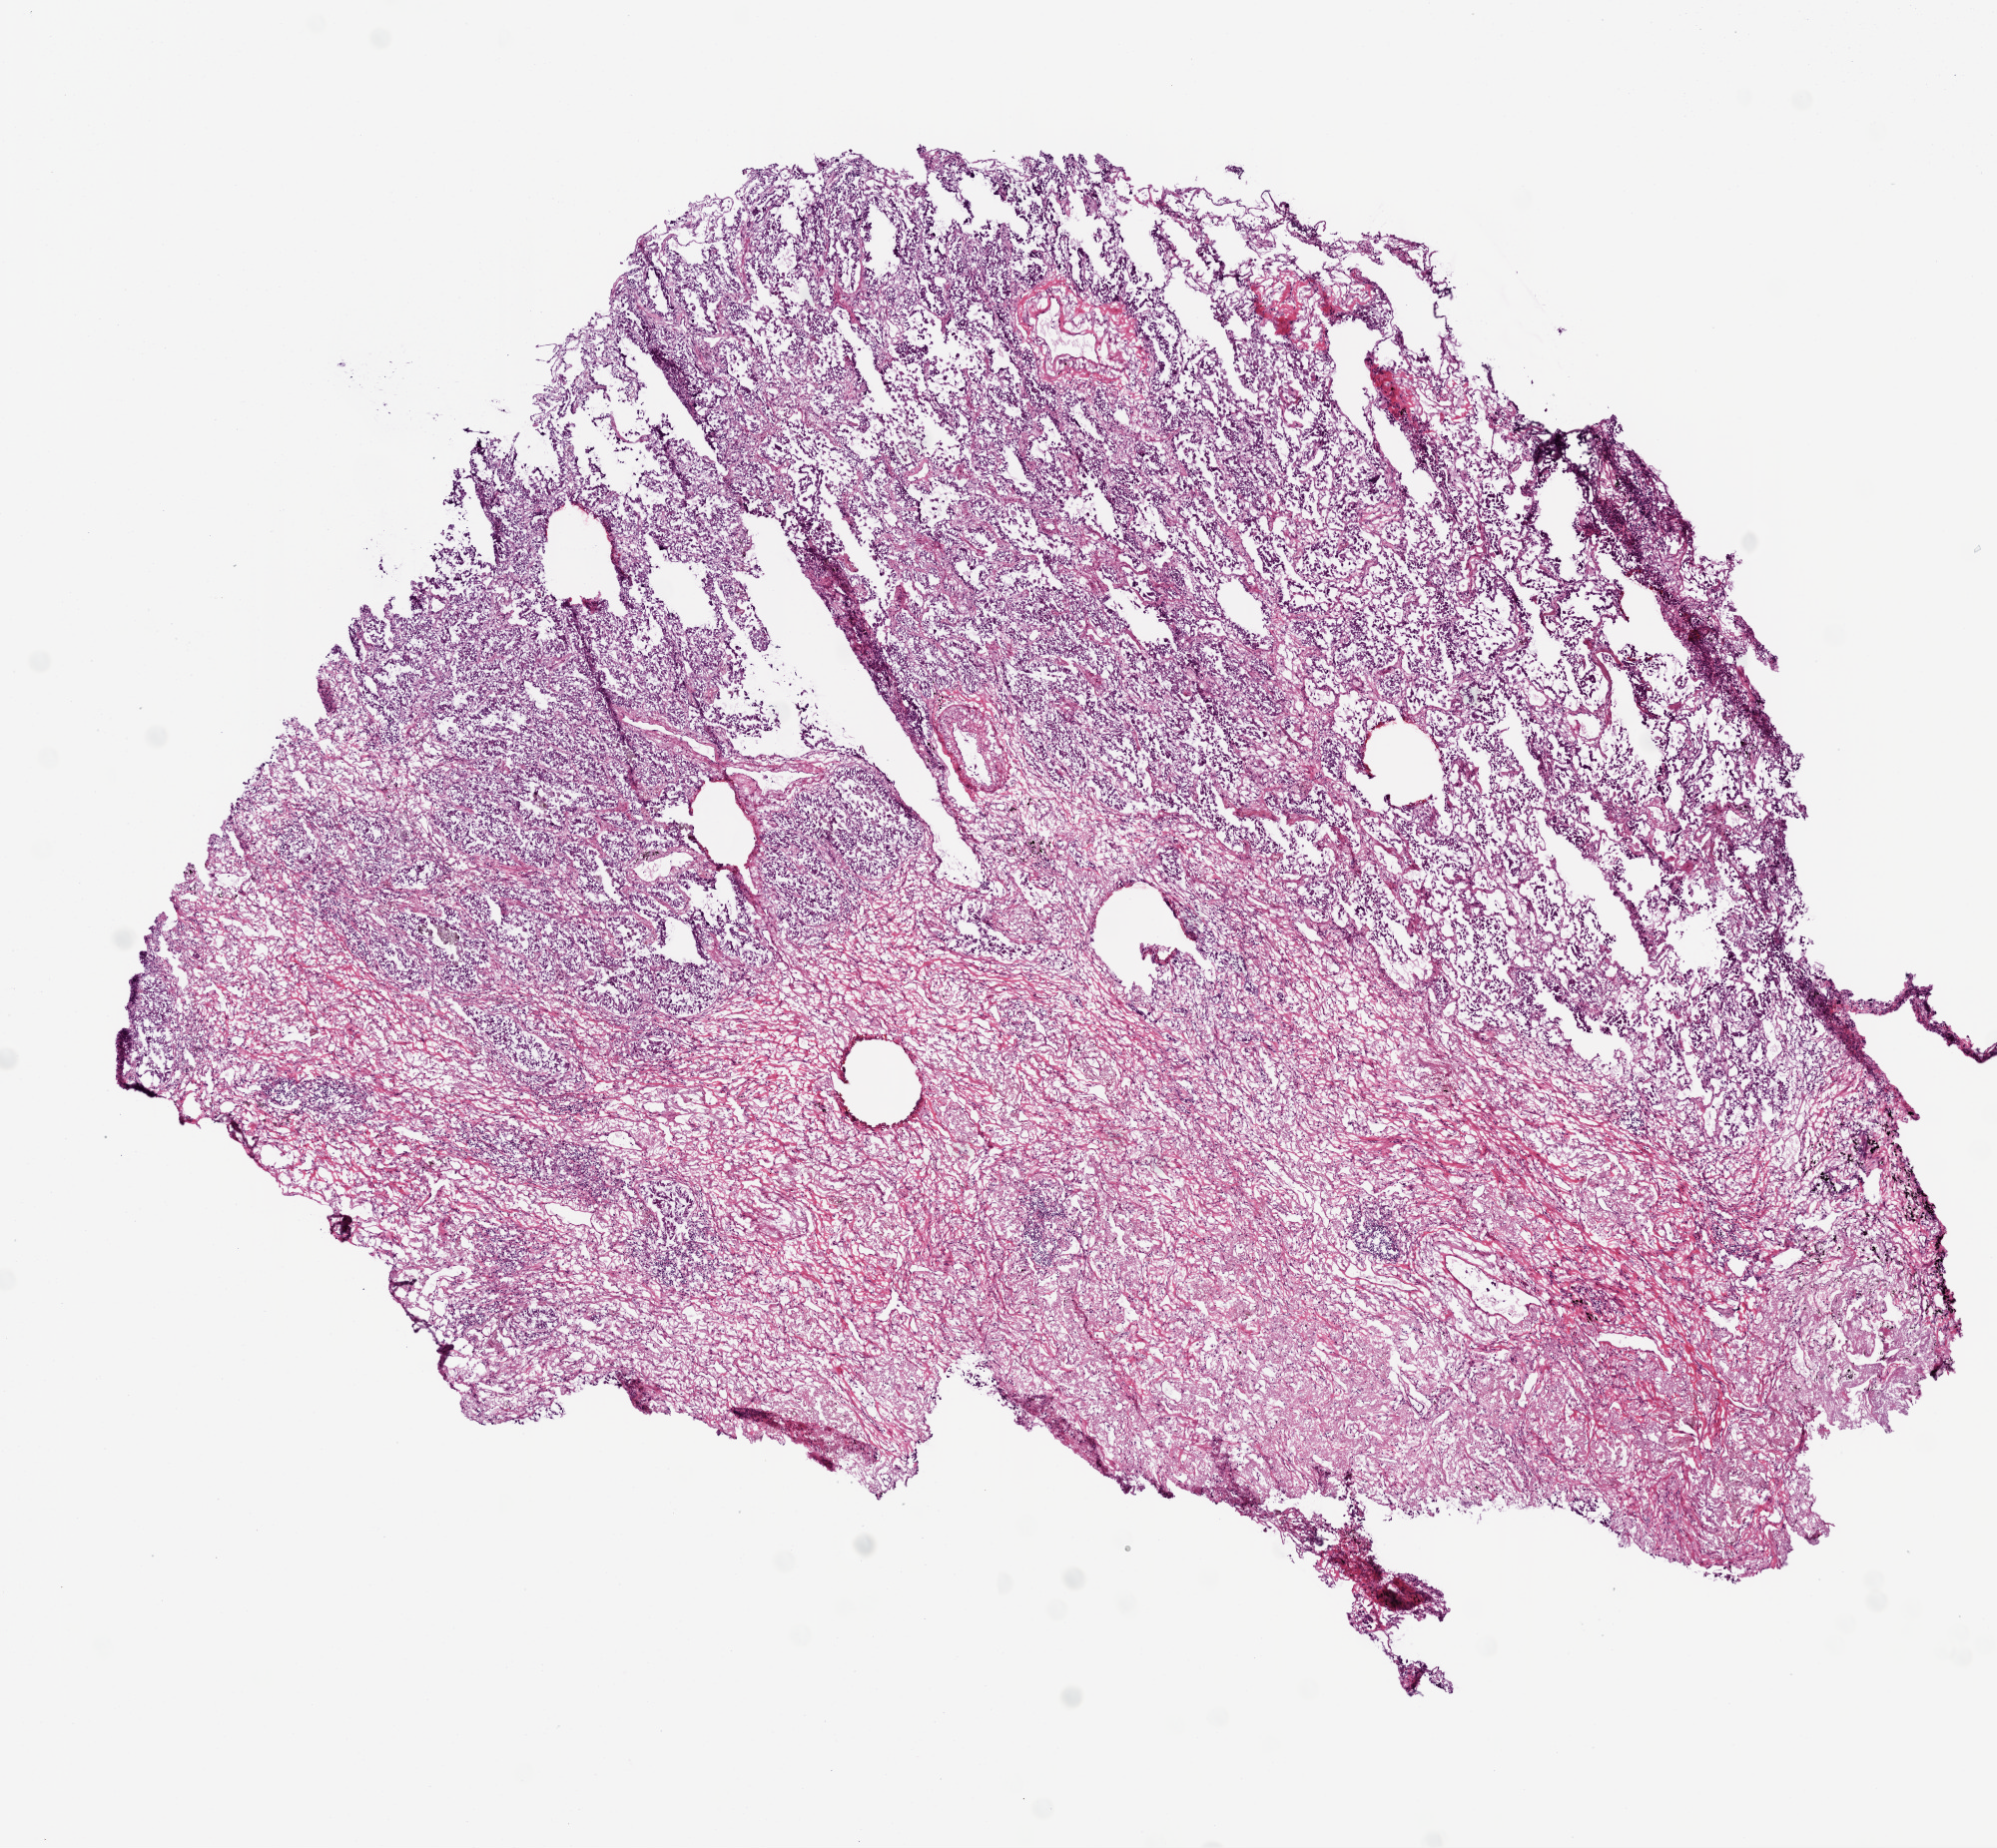
Whole-slide histology image, Hematoxylin and eosin (H&E) stained, whole scanned area (about 8.0 x 7.4 mm) shown as a low-resolution overview; frozen section; lung, primary tumour sample. Male patient; age at initial diagnosis 72 years. Composition of this section per pathologist review: tumour cells 100%, tumour nuclei 80%, normal cells 0%, stromal cells 0%, necrosis 0%. Inflammatory infiltration, as recorded: monocyte infiltration 5%.
Laterality: right. TNM: T1a N0 M0. AJCC pathologic stage: IA (7th edition). Histologic diagnosis: Acinar cell carcinoma (upper lobe, lung).